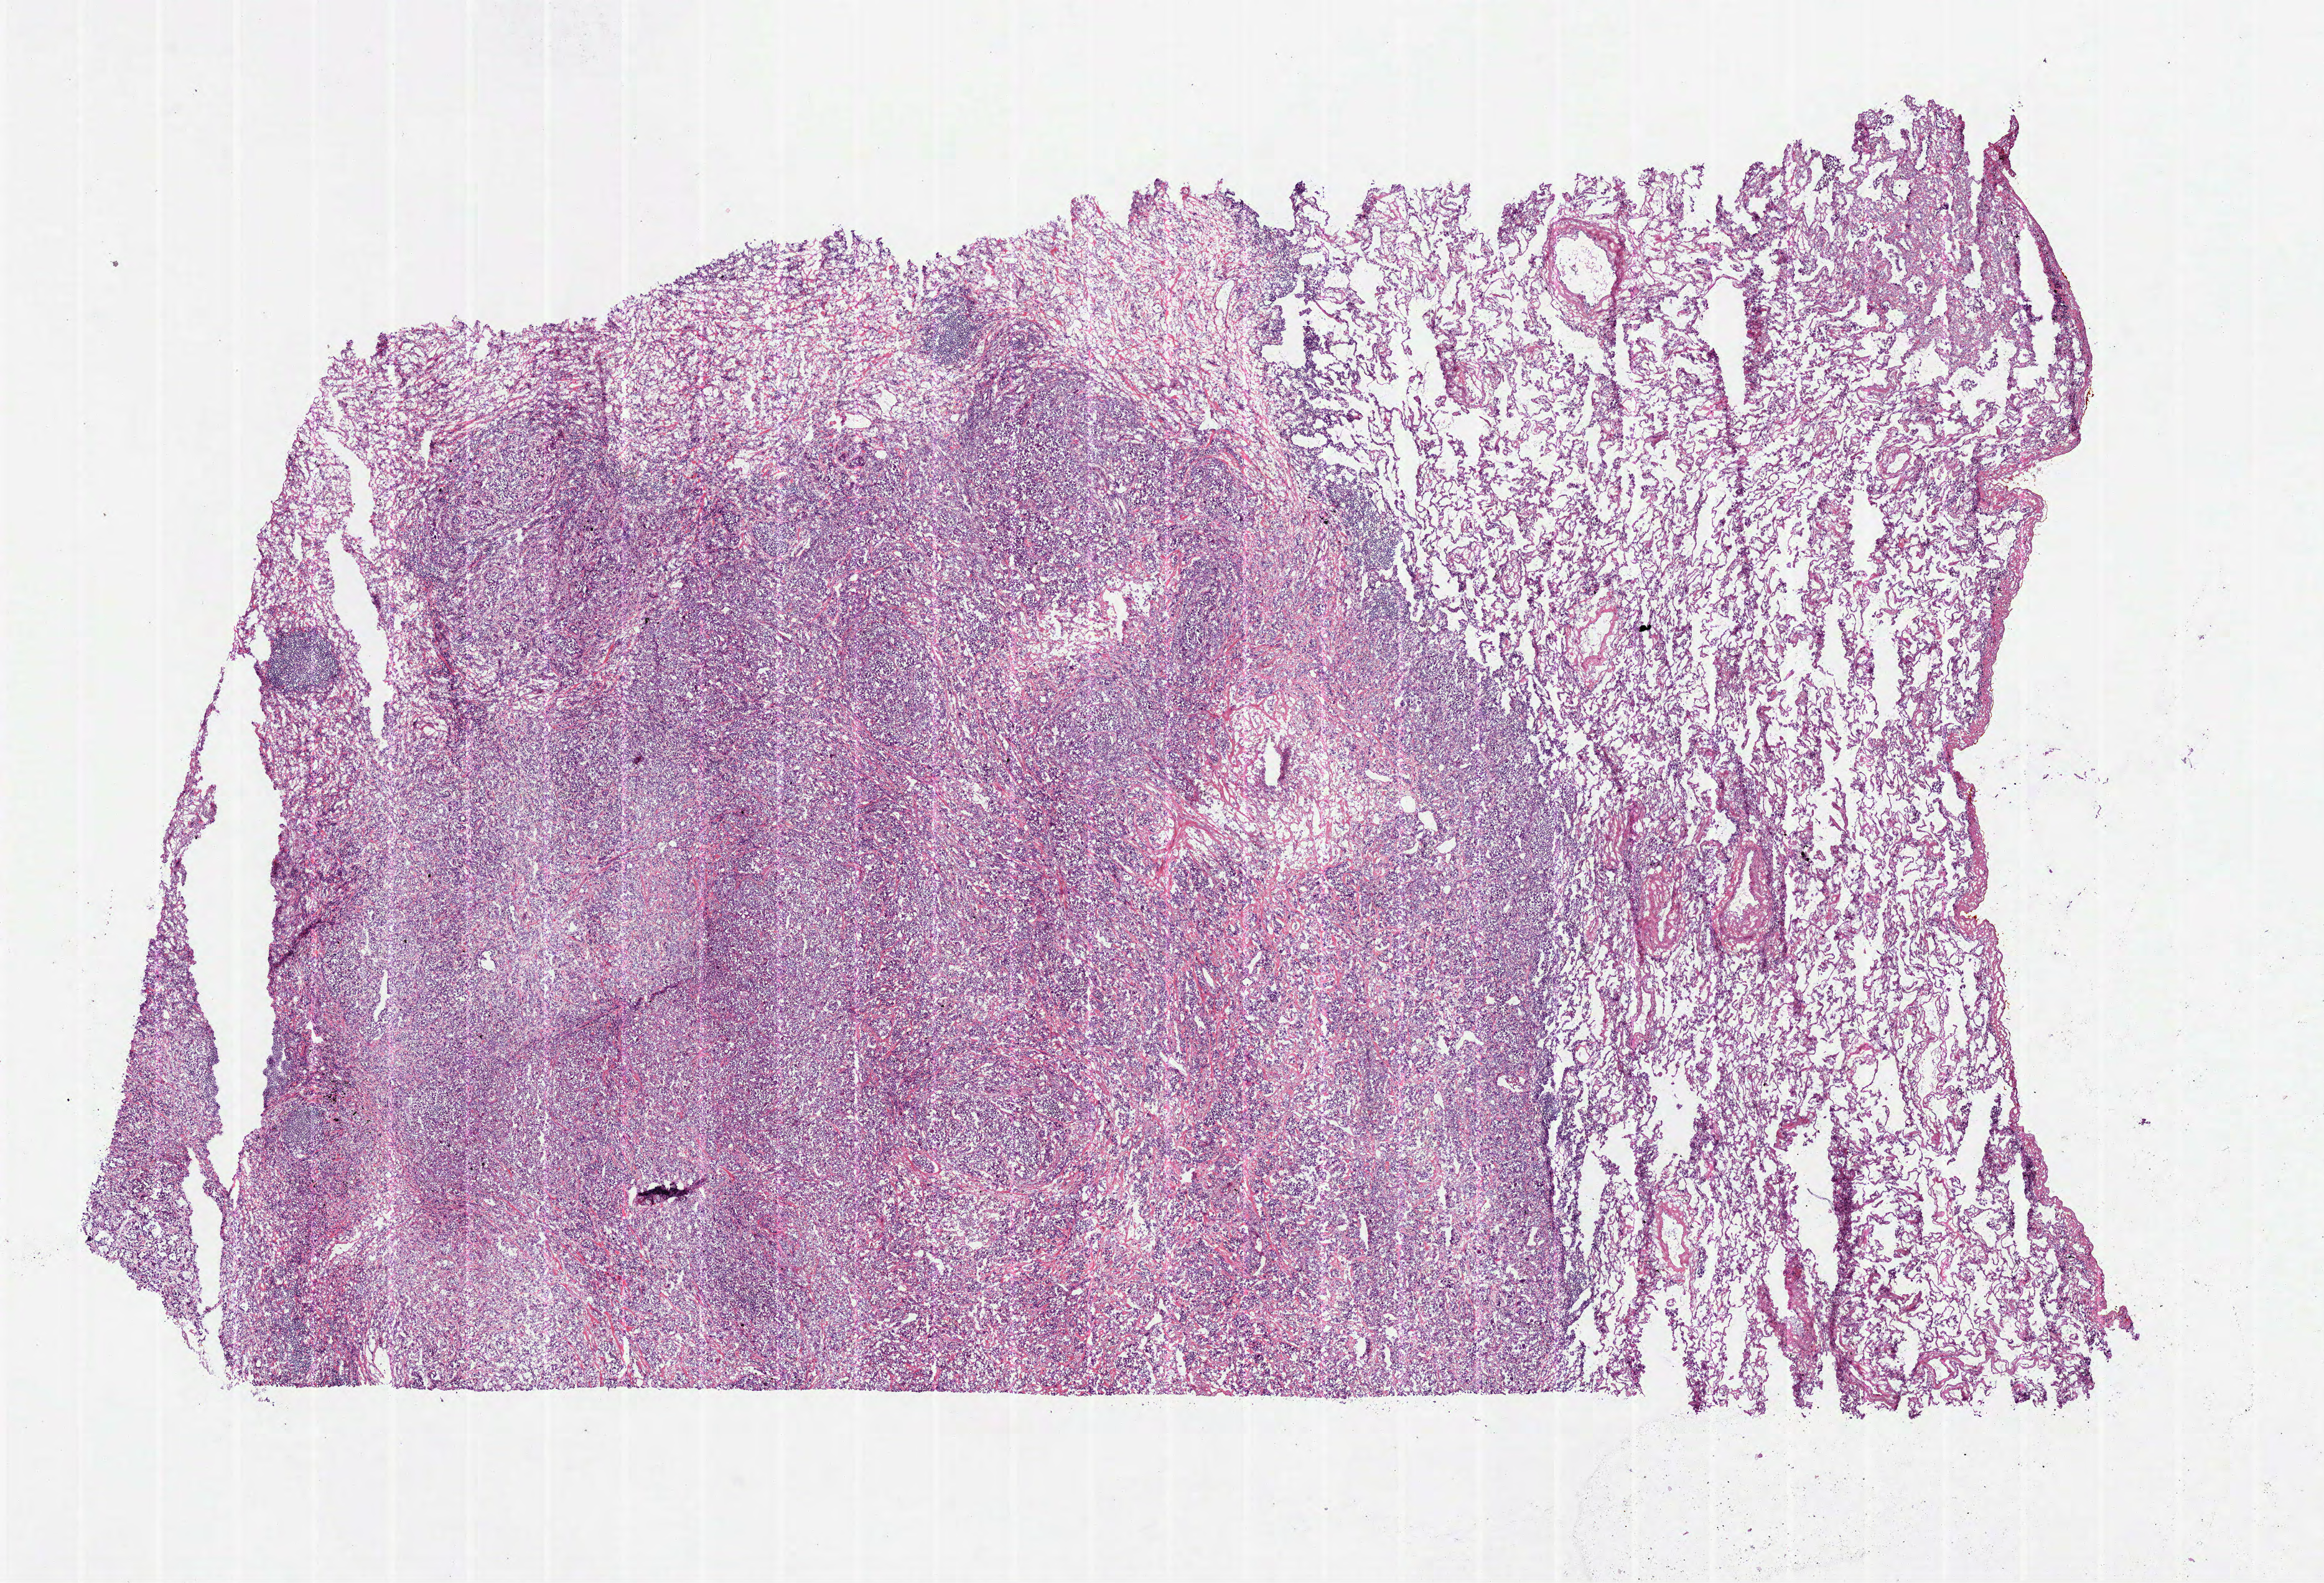
Whole-slide histology image, H&E-stained, shown as a low-resolution overview of the whole scanned area (about 15.1 x 10.3 mm, slide scanned at 40x). Frozen section from the bottom of the tissue portion. Sample: primary tumour, lung. Male, age 85 years at initial diagnosis. Pathologist review of this section (percent, as recorded): tumour cells 0%, tumour nuclei 71%, normal cells 0%, stromal cells 0%, necrosis 0%. Inflammatory infiltration, as recorded: lymphocyte infiltration 10%, monocyte infiltration 5%, neutrophil infiltration 10%.
AJCC pathologic stage: IB (6th edition). Pathologic diagnosis: Adenocarcinoma with mixed subtypes (upper lobe, lung).